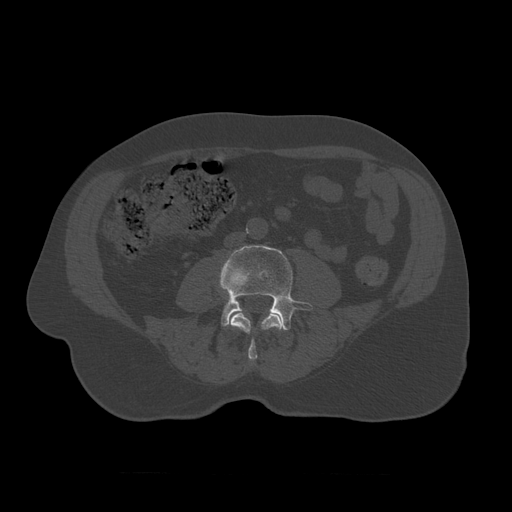
CT including the spine, one axial slice; position 286 of 450 along the scan axis; reconstruction kernel STANDARD; 120 kVp; bone window (W 1800 / L 400 HU); 512 × 512 image matrix, field of view 405 × 405 mm. Patient age 75 years. From the clinical record (not read from this slice): primary cancer: prostate.
Structures marked on this image (semi-automatically segmented with operator editing):
- L3 vertebra: bounding box [x1, y1, x2, y2] px = [230, 310, 285, 361]
- L4 vertebra: [220, 245, 313, 331]